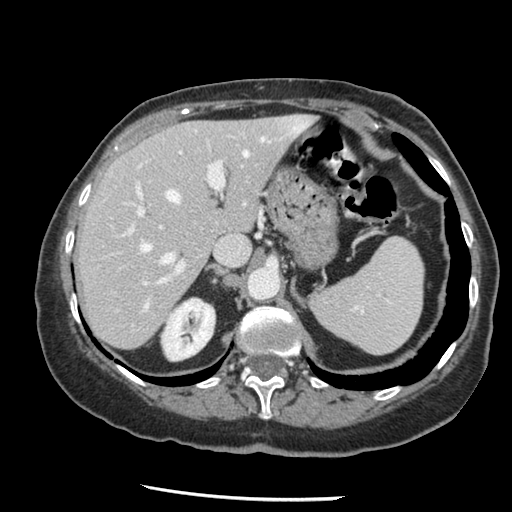
Contrast-enhanced abdominal CT, one axial slice. Slice 93 of 148 in the series (ordered by position). Reconstruction kernel STANDARD. Intravenous contrast given. Soft-tissue window (W 400 / L 40 HU). 2.5 mm slice thickness. 512 × 512 image matrix, field of view 330 × 330 mm. Female patient, age 85 years. Case-level facts recorded for this patient, not image findings: diagnosis: colorectal cancer liver metastases, imaged before liver resection.
Annotated regions visible in this slice (expert manual segmentation):
- hepatic veins: bounding box <141,134,297,309> (left, top, right, bottom; pixels)
- liver: <79,116,313,348>
- planned liver remnant (the part of the liver to remain after resection): <79,116,313,348>
- portal vein (with intrahepatic branches): <122,140,225,285>